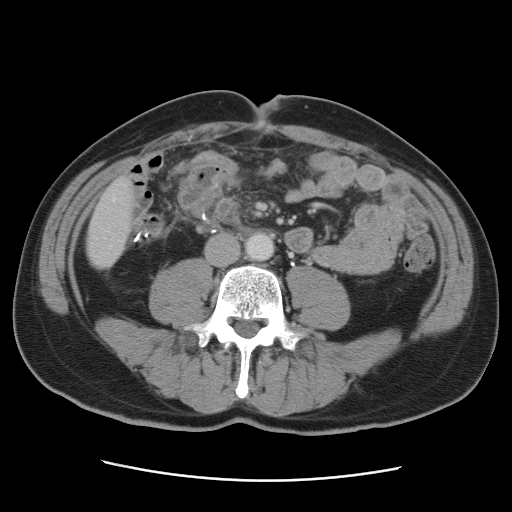
Contrast-enhanced abdominal CT, one axial slice; position 9 of 89 along the scan axis; 120 kVp; intravenous contrast given; soft-tissue window (W 400 / L 40 HU); 512 × 512 image matrix. Male patient, age 59 years. From the clinical record (not read from this slice): diagnosis: colorectal cancer liver metastases, imaged before liver resection; multiple liver metastases: yes; largest metastasis: 0.6 cm.
Structures marked on this image (expert manual segmentation):
- hepatic veins: bounding box (x1, y1, x2, y2) in pixels: (113, 199, 115, 201)
- liver: (87, 180, 134, 267)
- planned liver remnant (the part of the liver to remain after resection): (87, 180, 134, 258)